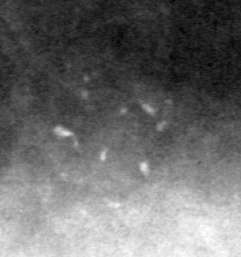
Cropped region of a digitized screen-film mammogram centred on a radiologist-marked abnormality; right breast; CC view; BI-RADS breast density category 4 (scale 1–4).
- Finding: calcifications, morphology pleomorphic, distribution clustered; BI-RADS assessment category 4; pathology result (as recorded, not read from the image): benign.